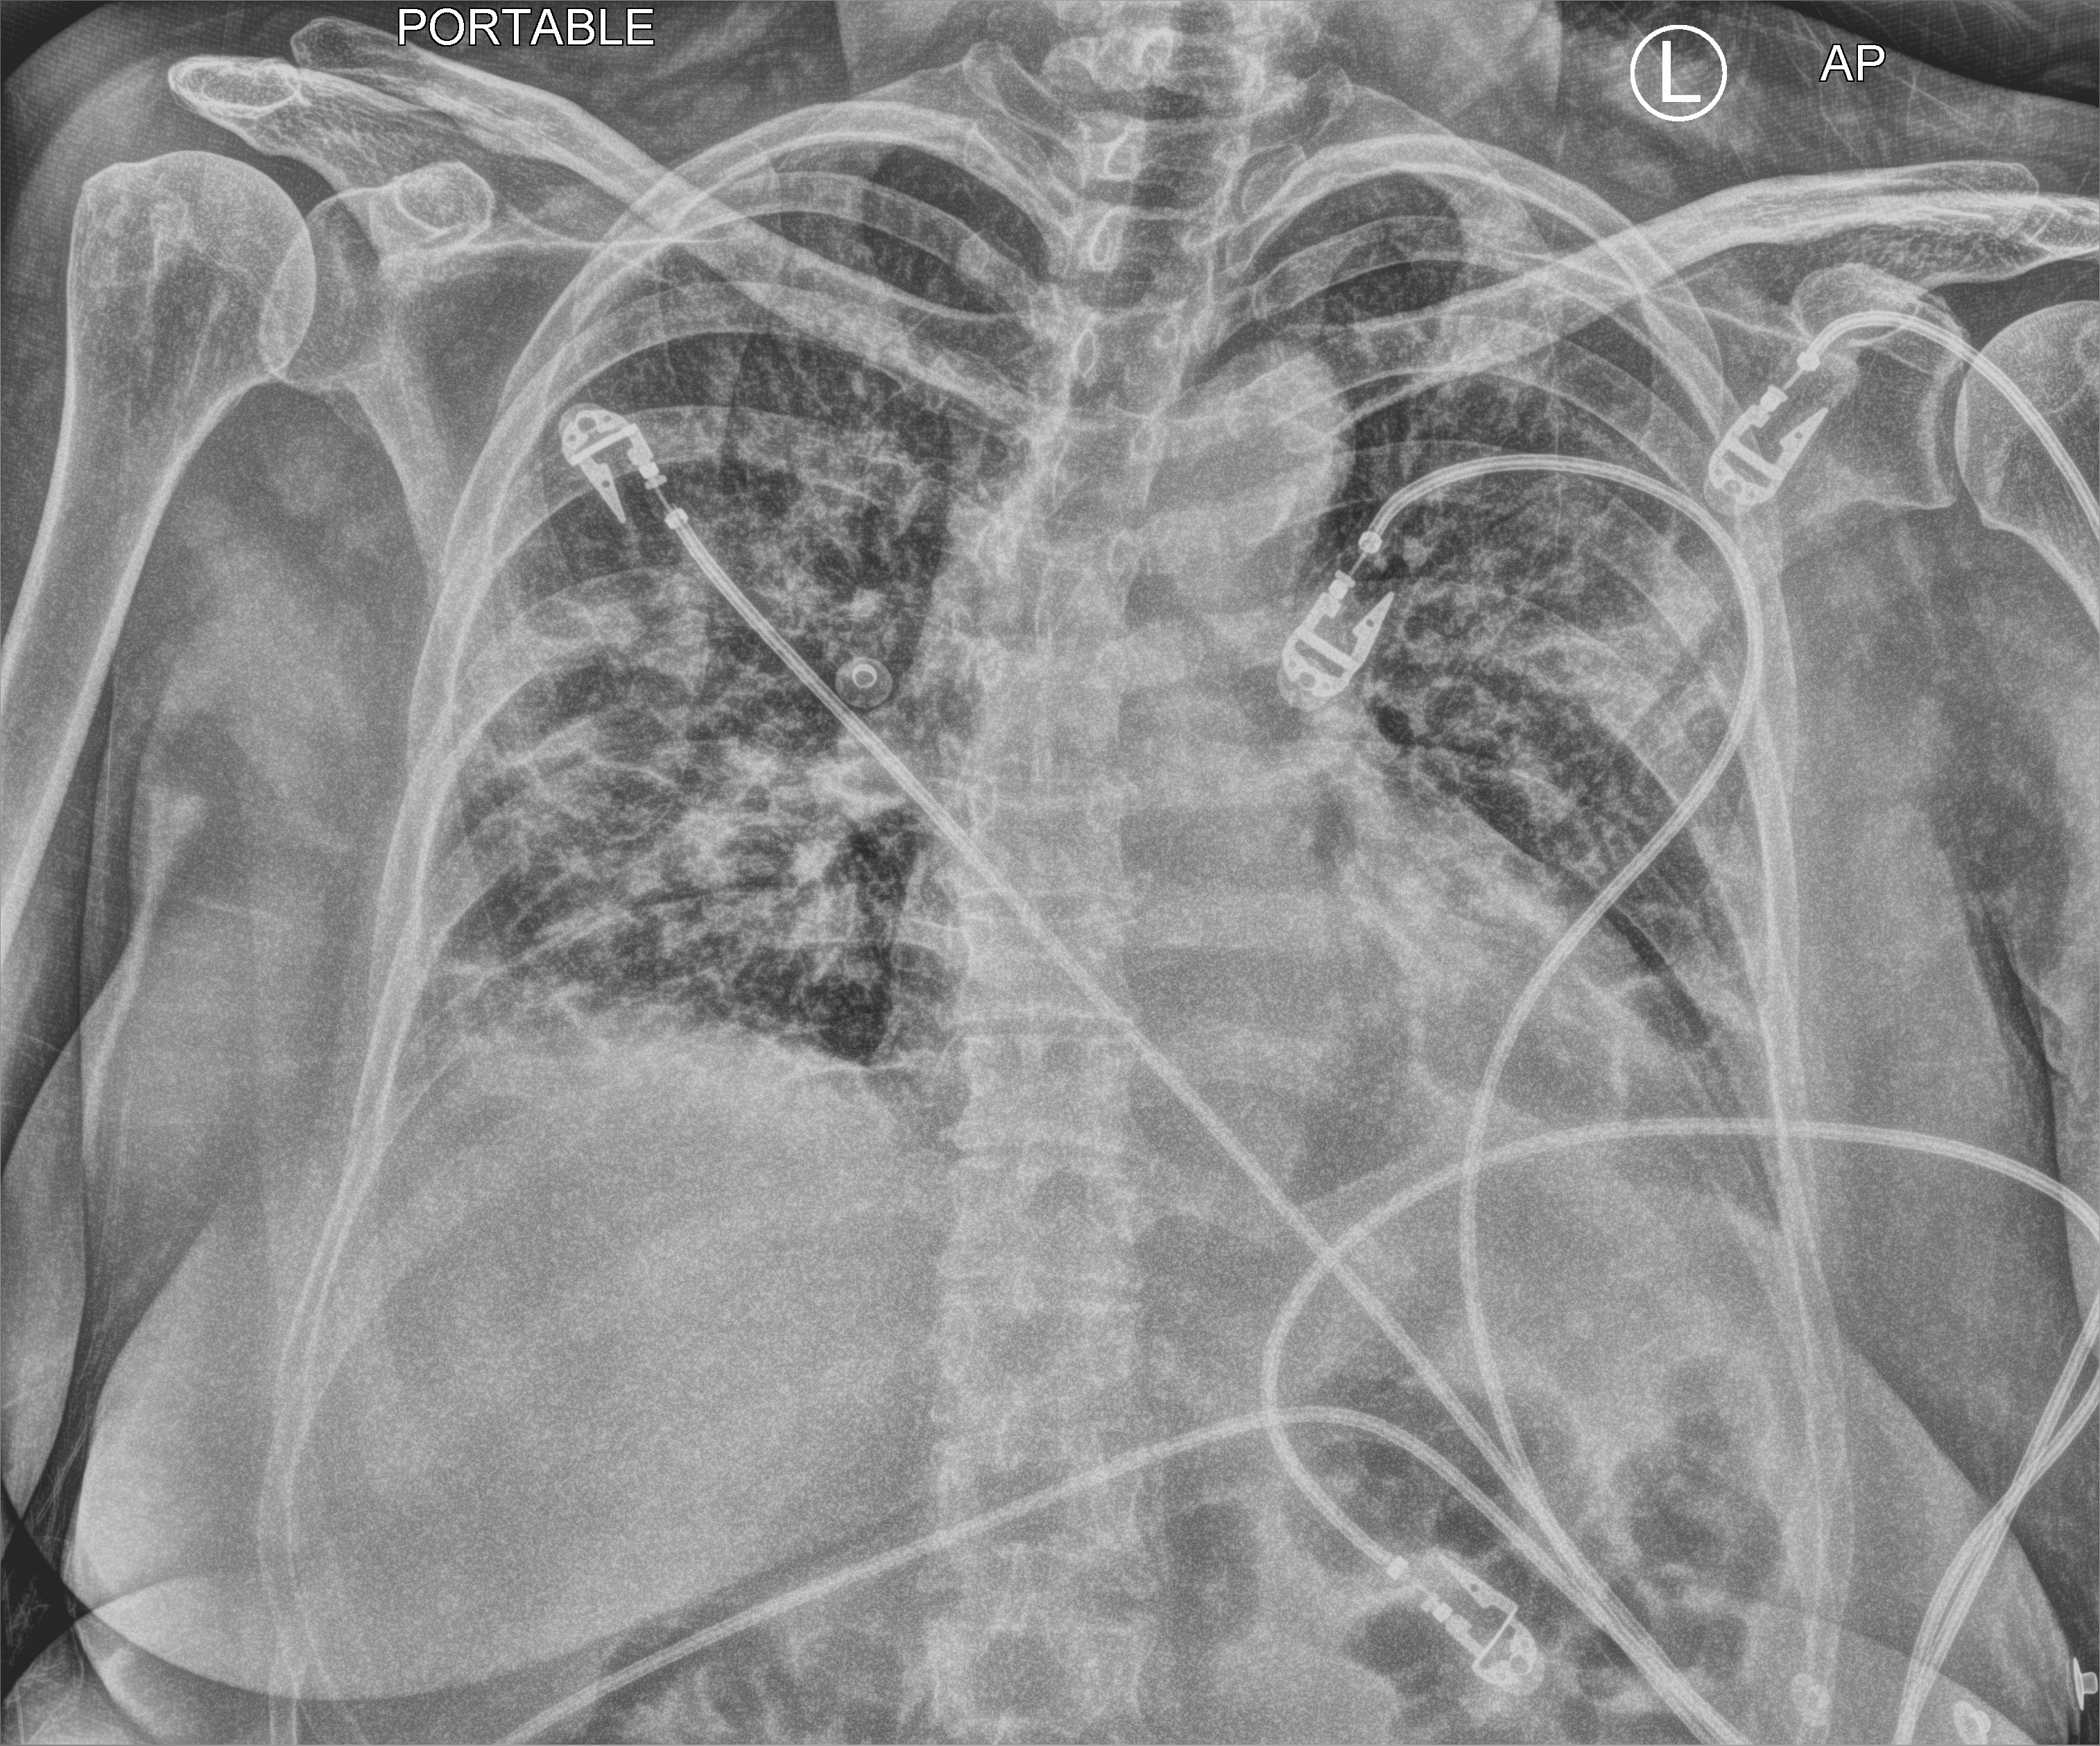
Chest X-ray (portable); anteroposterior (AP) projection. Female patient hospitalised with COVID-19, age 60–74 years.
From the hospital-stay record, not from the radiograph (when in the stay this image was taken is not recorded):
- admitted to intensive care during this hospital stay: no
- length of hospital stay: 8 days